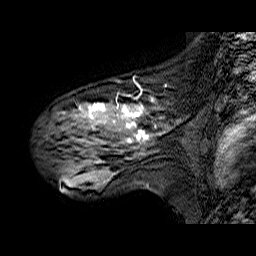
Breast MRI (dynamic contrast-enhanced), one sagittal slice; position 41 of 60 along the scan axis; dynamic contrast-enhanced series, time point 2 of 6 at this slice position (early post-contrast); 1.5 T; TE 6.3 ms, TR 32.9 ms; 4 mm slice thickness; 256 × 256 image matrix, field of view 200 × 200 mm. Female patient. Case-level facts recorded for this patient, not image findings: setting: breast cancer imaged before/during neoadjuvant chemotherapy; receptor status: HER2-positive.
Outlined on this slice (semi-automatically segmented with operator editing):
- analysis volume of interest (the breast-tissue region the enhancement analysis was run in; not a lesion): box from (x=45, y=85) to (x=174, y=173) px
- tumour enhancement mask (voxels above the 100 % enhancement threshold inside the analysis volume of interest): (x=89, y=103)–(x=150, y=142)